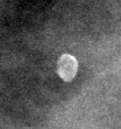
Region of interest cut from a scanned film mammogram (one marked finding); right breast; CC view.
- Finding: calcifications, morphology round and regular / lucent centered; BI-RADS assessment category 2; subtlety rating 3 on a 1 (subtle) to 5 (obvious) scale; benign without callback (not worked up further).